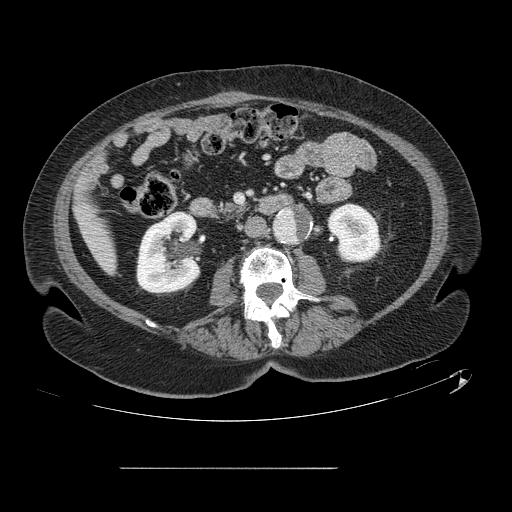
Contrast-enhanced abdominal CT, one axial slice. Slice 27 of 148 in the series (ordered by position). 120 kVp. Soft-tissue window (W 400 / L 40 HU). 2.5 mm slice thickness. 512 × 512 image matrix, field of view 439 × 439 mm. Female patient, age 75 years. From the clinical record (not read from this slice): diagnosis: colorectal cancer liver metastases, imaged before liver resection; multiple liver metastases: no; largest metastasis: 2.4 cm; disease in both lobes: no.
Outlined on this slice (outlined manually by an expert reader):
- liver: bounding box <77,193,116,271> (left, top, right, bottom; pixels)
- planned liver remnant (the part of the liver to remain after resection): <77,190,116,271>